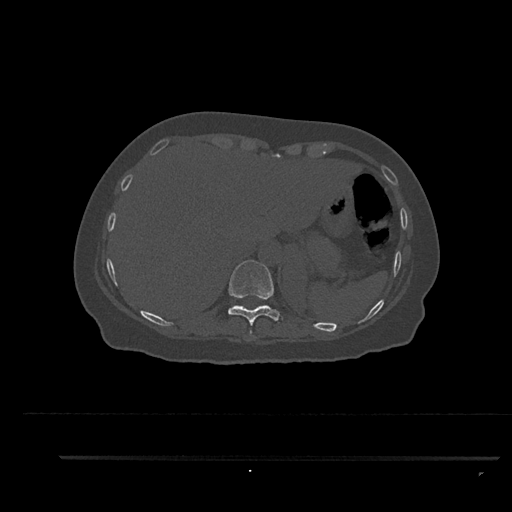
CT including the spine, one axial slice. Slice 362 of 797 in the series (ordered by position). 120 kVp. Bone window (W 1800 / L 400 HU). 0.5 mm slice thickness. 512 × 512 image matrix, field of view 408 × 408 mm. Patient: female, 44 years. From the clinical record (not read from this slice): primary cancer: renal.
Annotated regions visible in this slice (semi-automatically segmented with operator editing):
- T10 vertebra: bounding box <228,260,283,335> (left, top, right, bottom; pixels)
- T9 vertebra: <250,330,254,336>